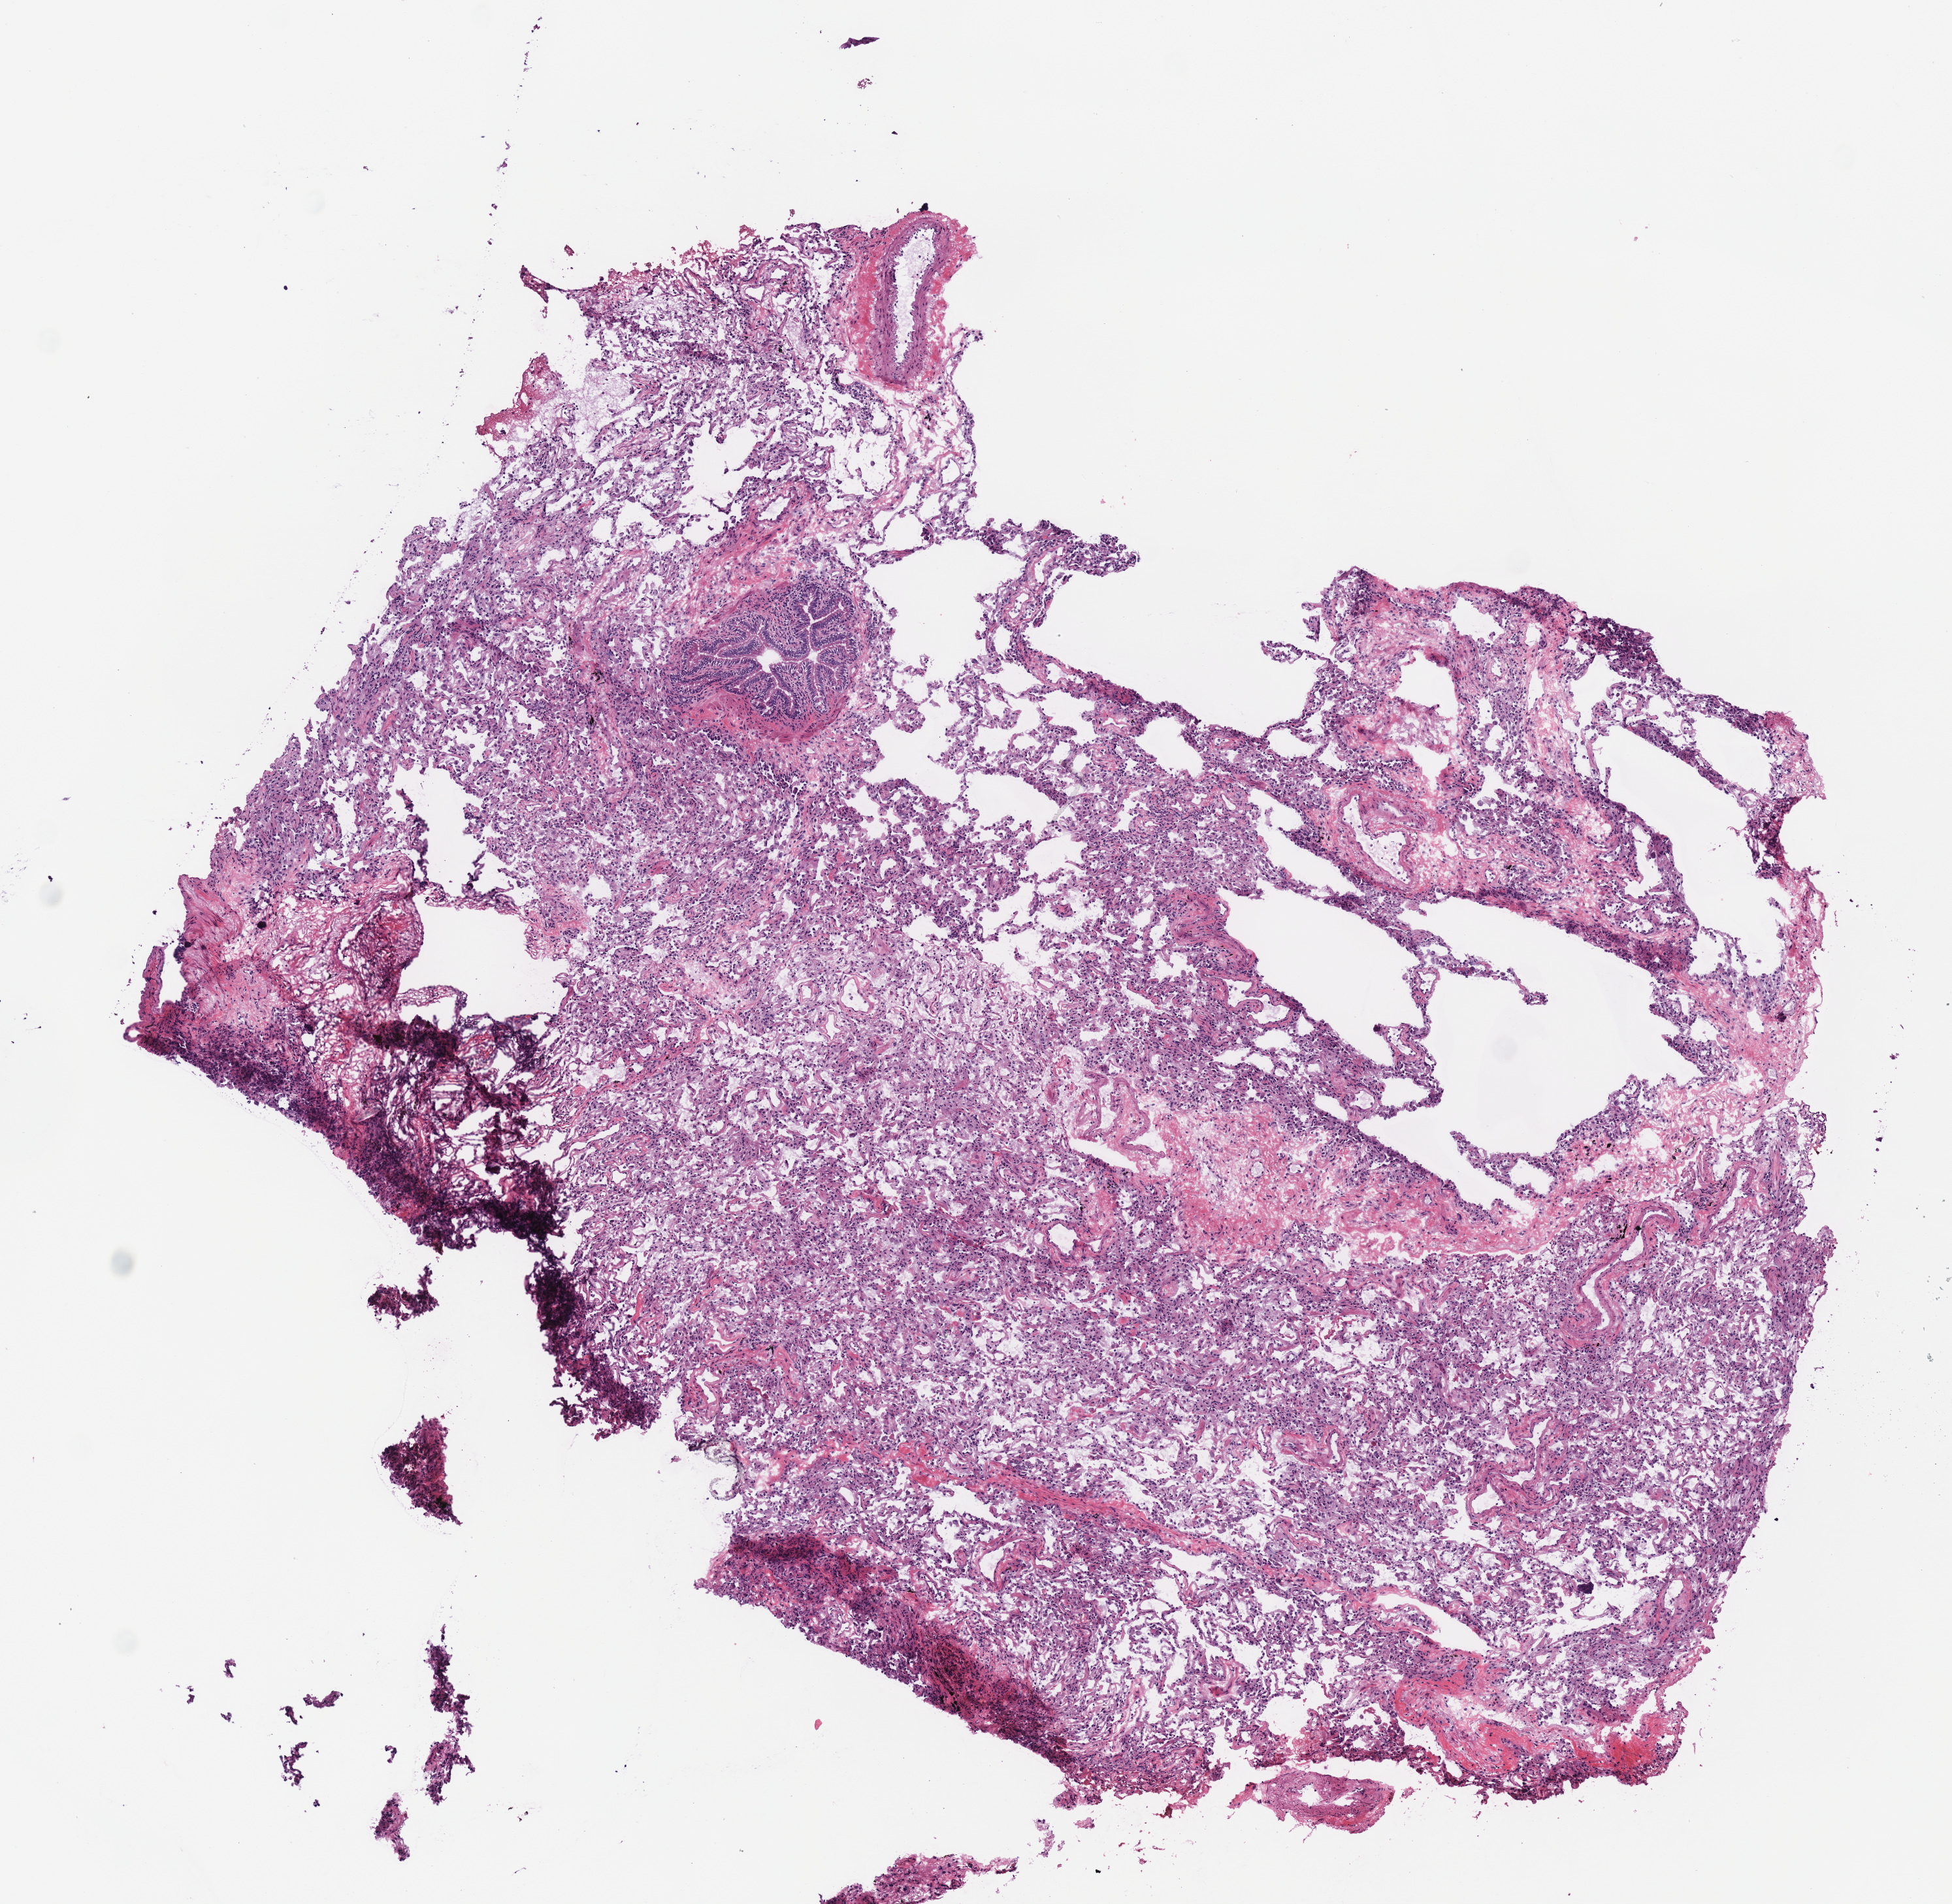
Hematoxylin and eosin (H&E) stained whole-slide image, whole scanned area (about 5.9 x 5.7 mm) shown as a low-resolution overview. Frozen section from the top of the tissue portion. Sample: solid tissue normal (non-tumour tissue), lung. Female, age 77 years at initial diagnosis.
This section: solid tissue normal sample (biorepository sample class). Patient diagnosis: Squamous cell carcinoma, NOS (lower lobe, lung).